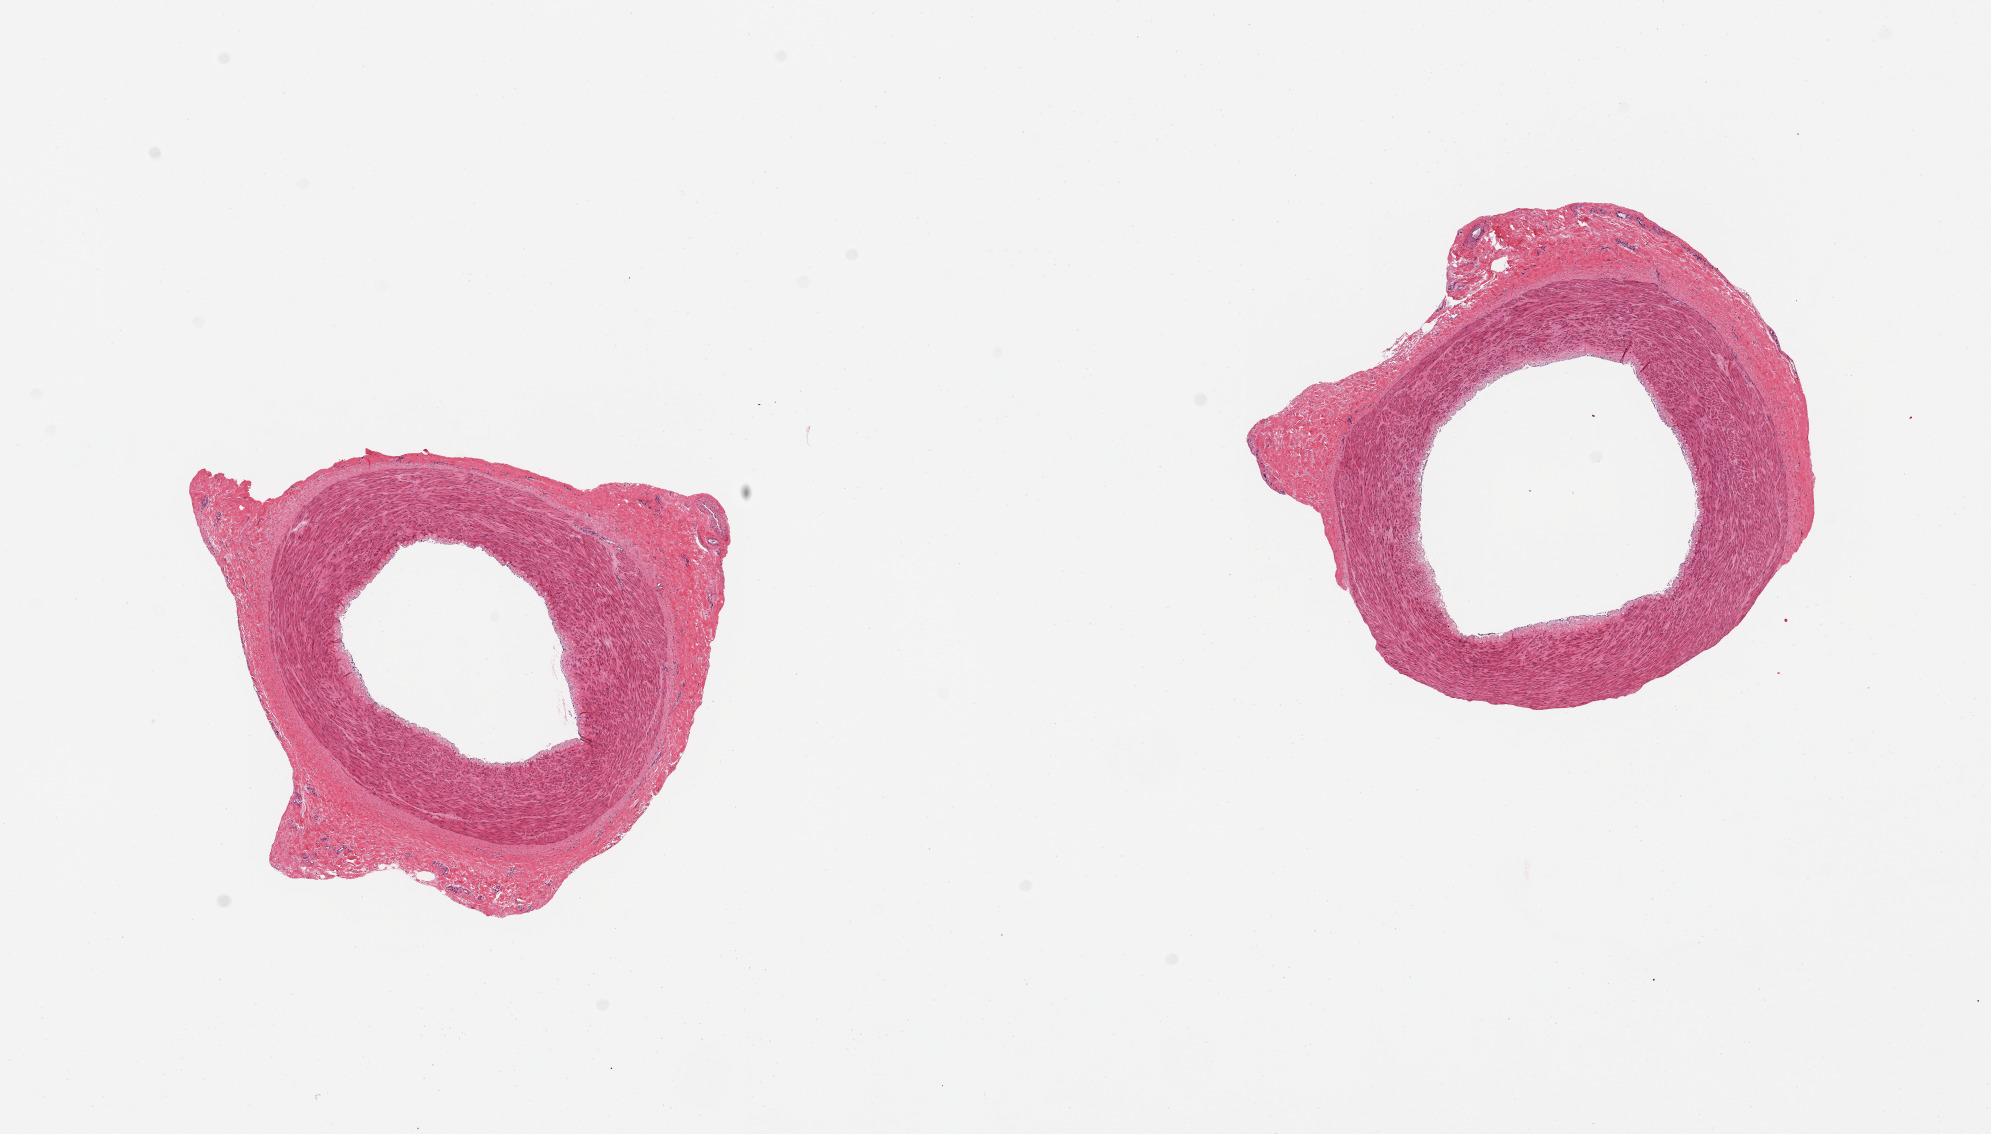
Whole-slide image, H&E stain — shown as a low-resolution overview of the whole scanned area (about 15.8 x 9.0 mm), PAXgene-fixed paraffin-embedded (PFPE) section, section of tibial artery (target tissue), tissue donor sample.
• review note (as recorded): 2 pieces; well trimmed; no lesions